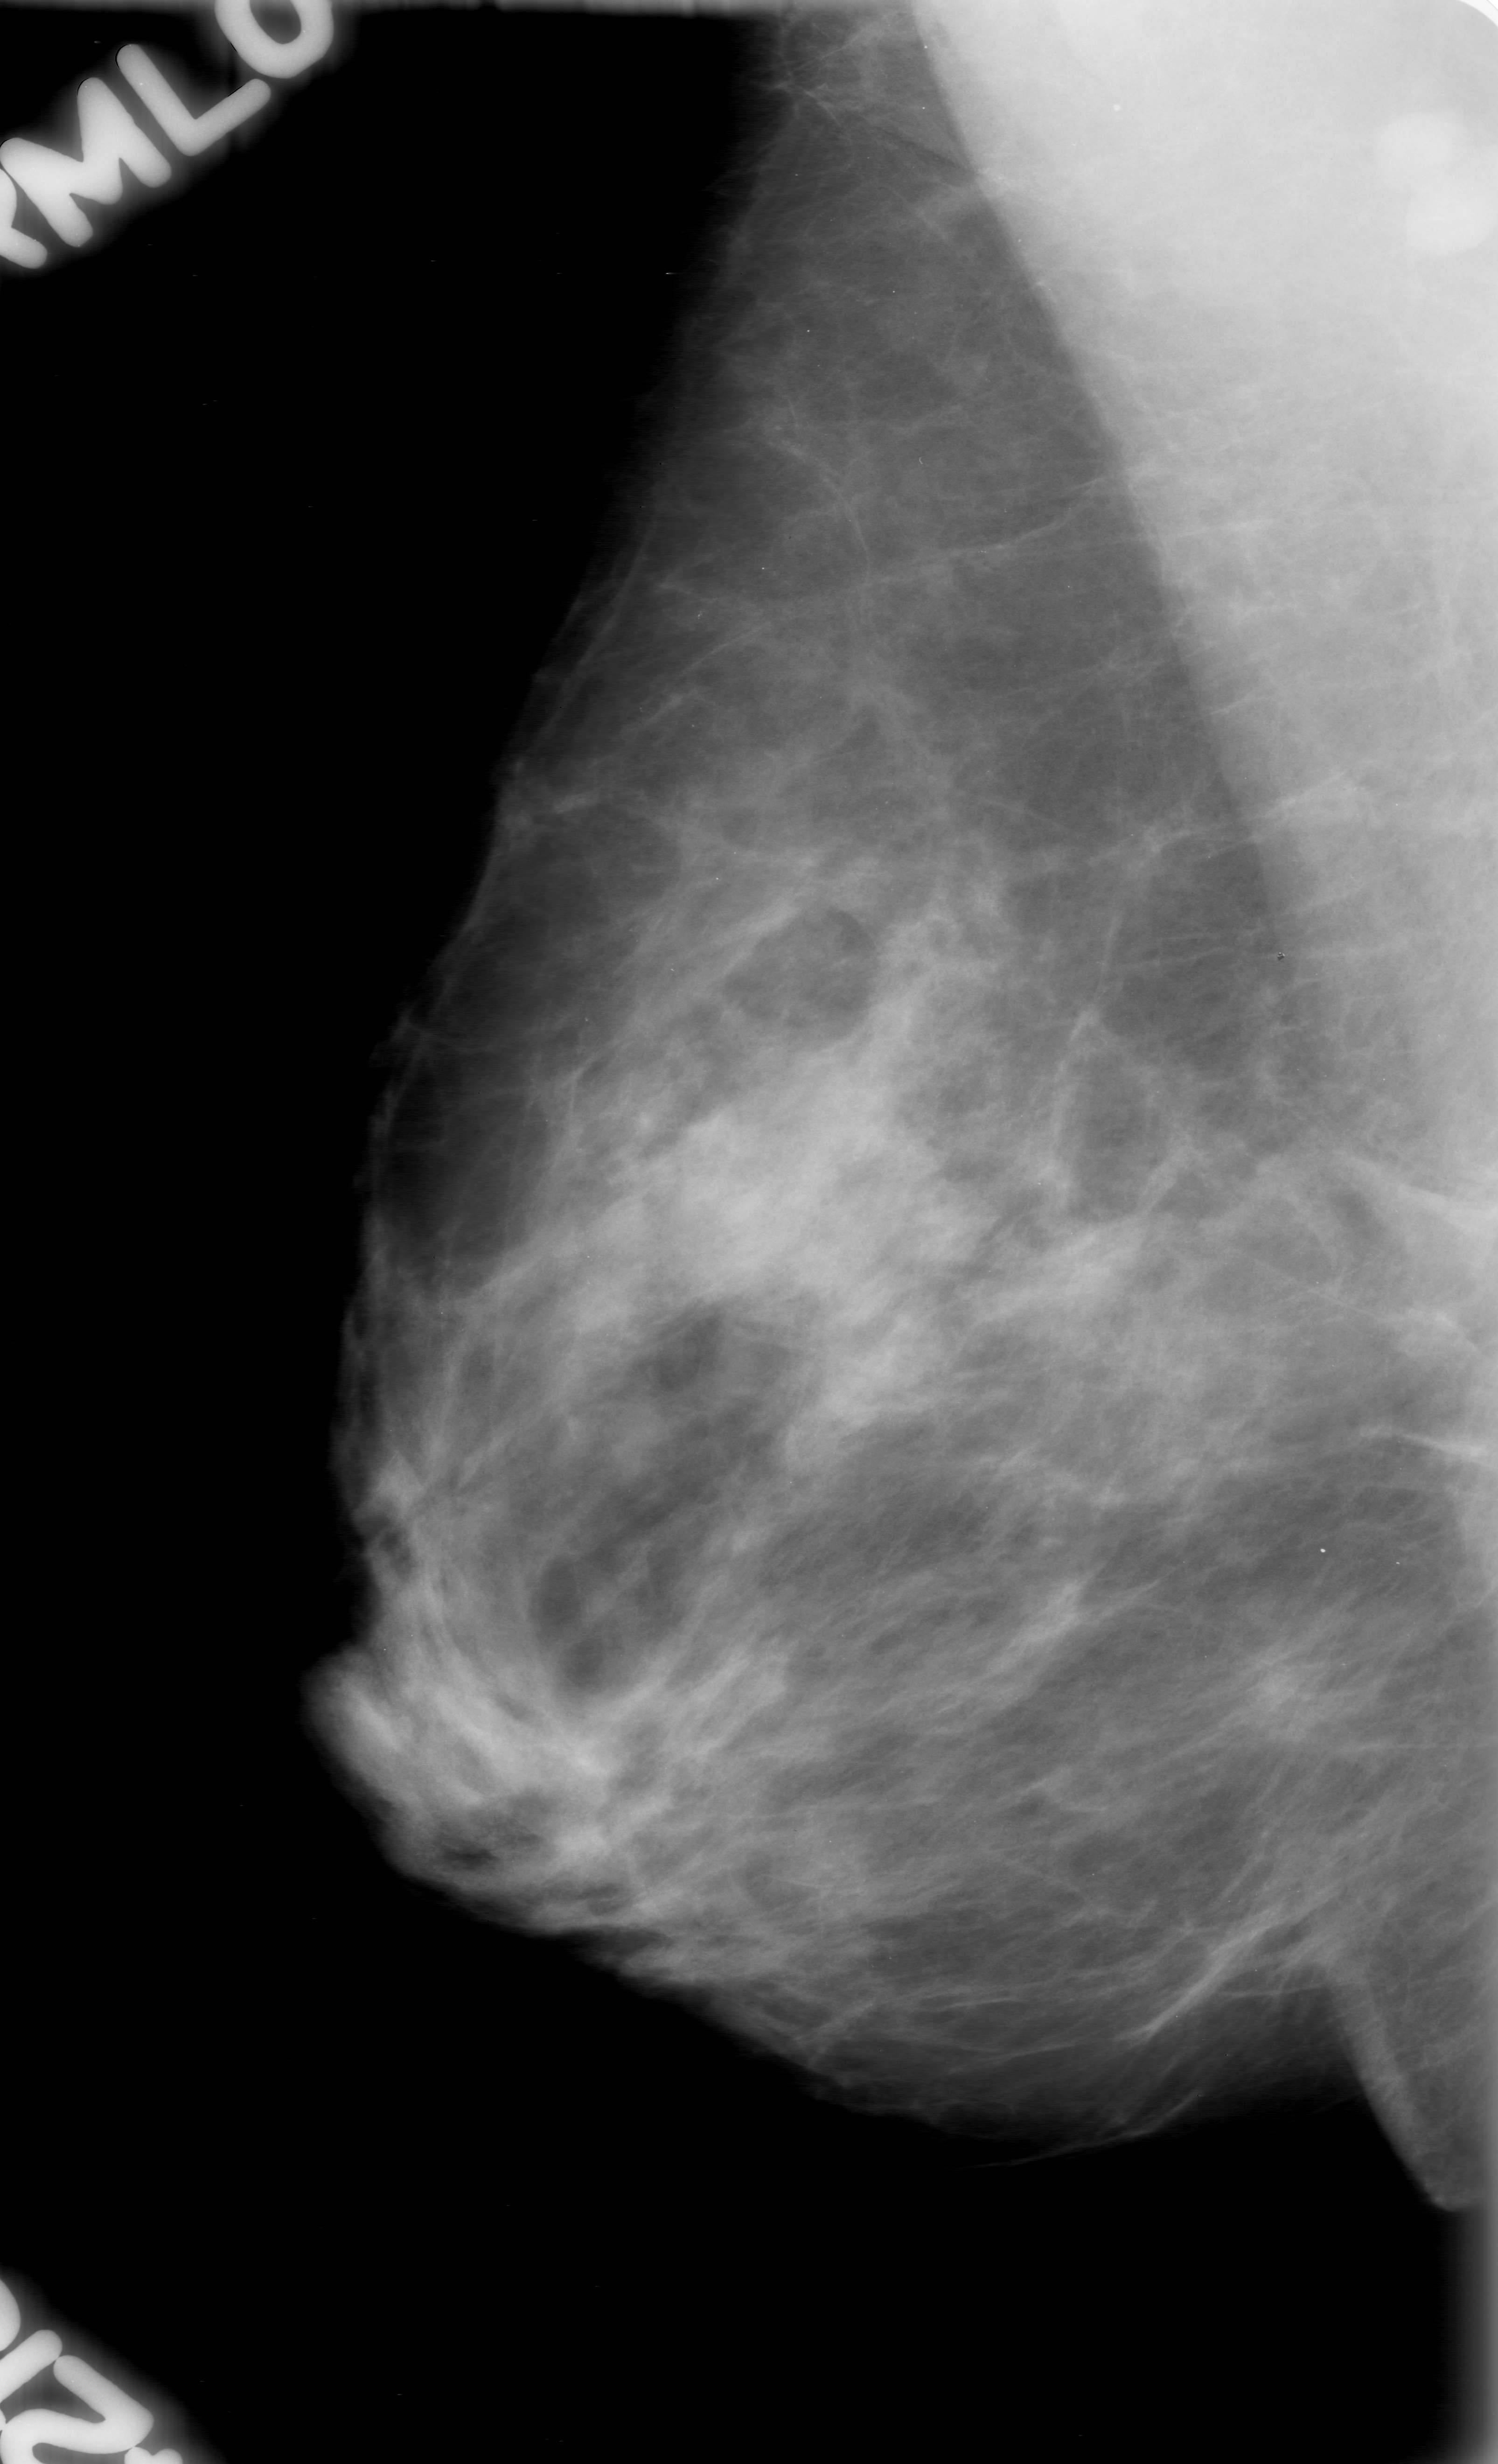
Scanned film-screen mammogram, right breast, mediolateral oblique (MLO) view, BI-RADS breast density category 2 (scale 1–4).
Finding: mass, shape oval, margins obscured; BI-RADS assessment category 0 (incomplete: needs additional imaging); pathology result (as recorded, not read from the image): benign.